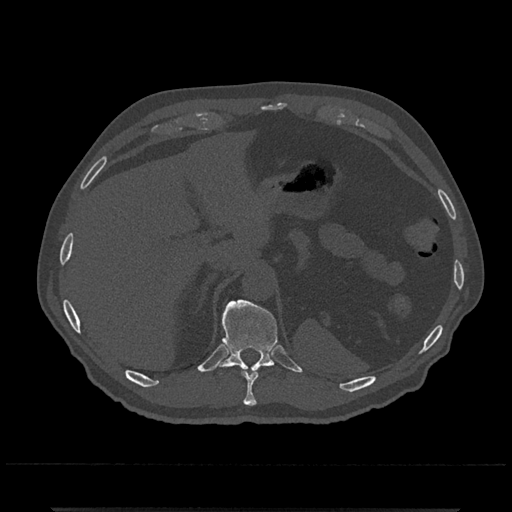
CT including the spine, one axial slice. Slice 513 of 797 in the series (ordered by position). 120 kVp. Bone window (W 1800 / L 400 HU). 512 × 512 image matrix, field of view 393 × 393 mm. Male patient, age 67 years. From the clinical record (not read from this slice): primary cancer: prostate.
Annotated regions visible in this slice (semi-automatically segmented with operator editing):
- T10 vertebra: box from (x=242, y=371) to (x=258, y=406) px
- T11 vertebra: (x=216, y=299)–(x=278, y=375)